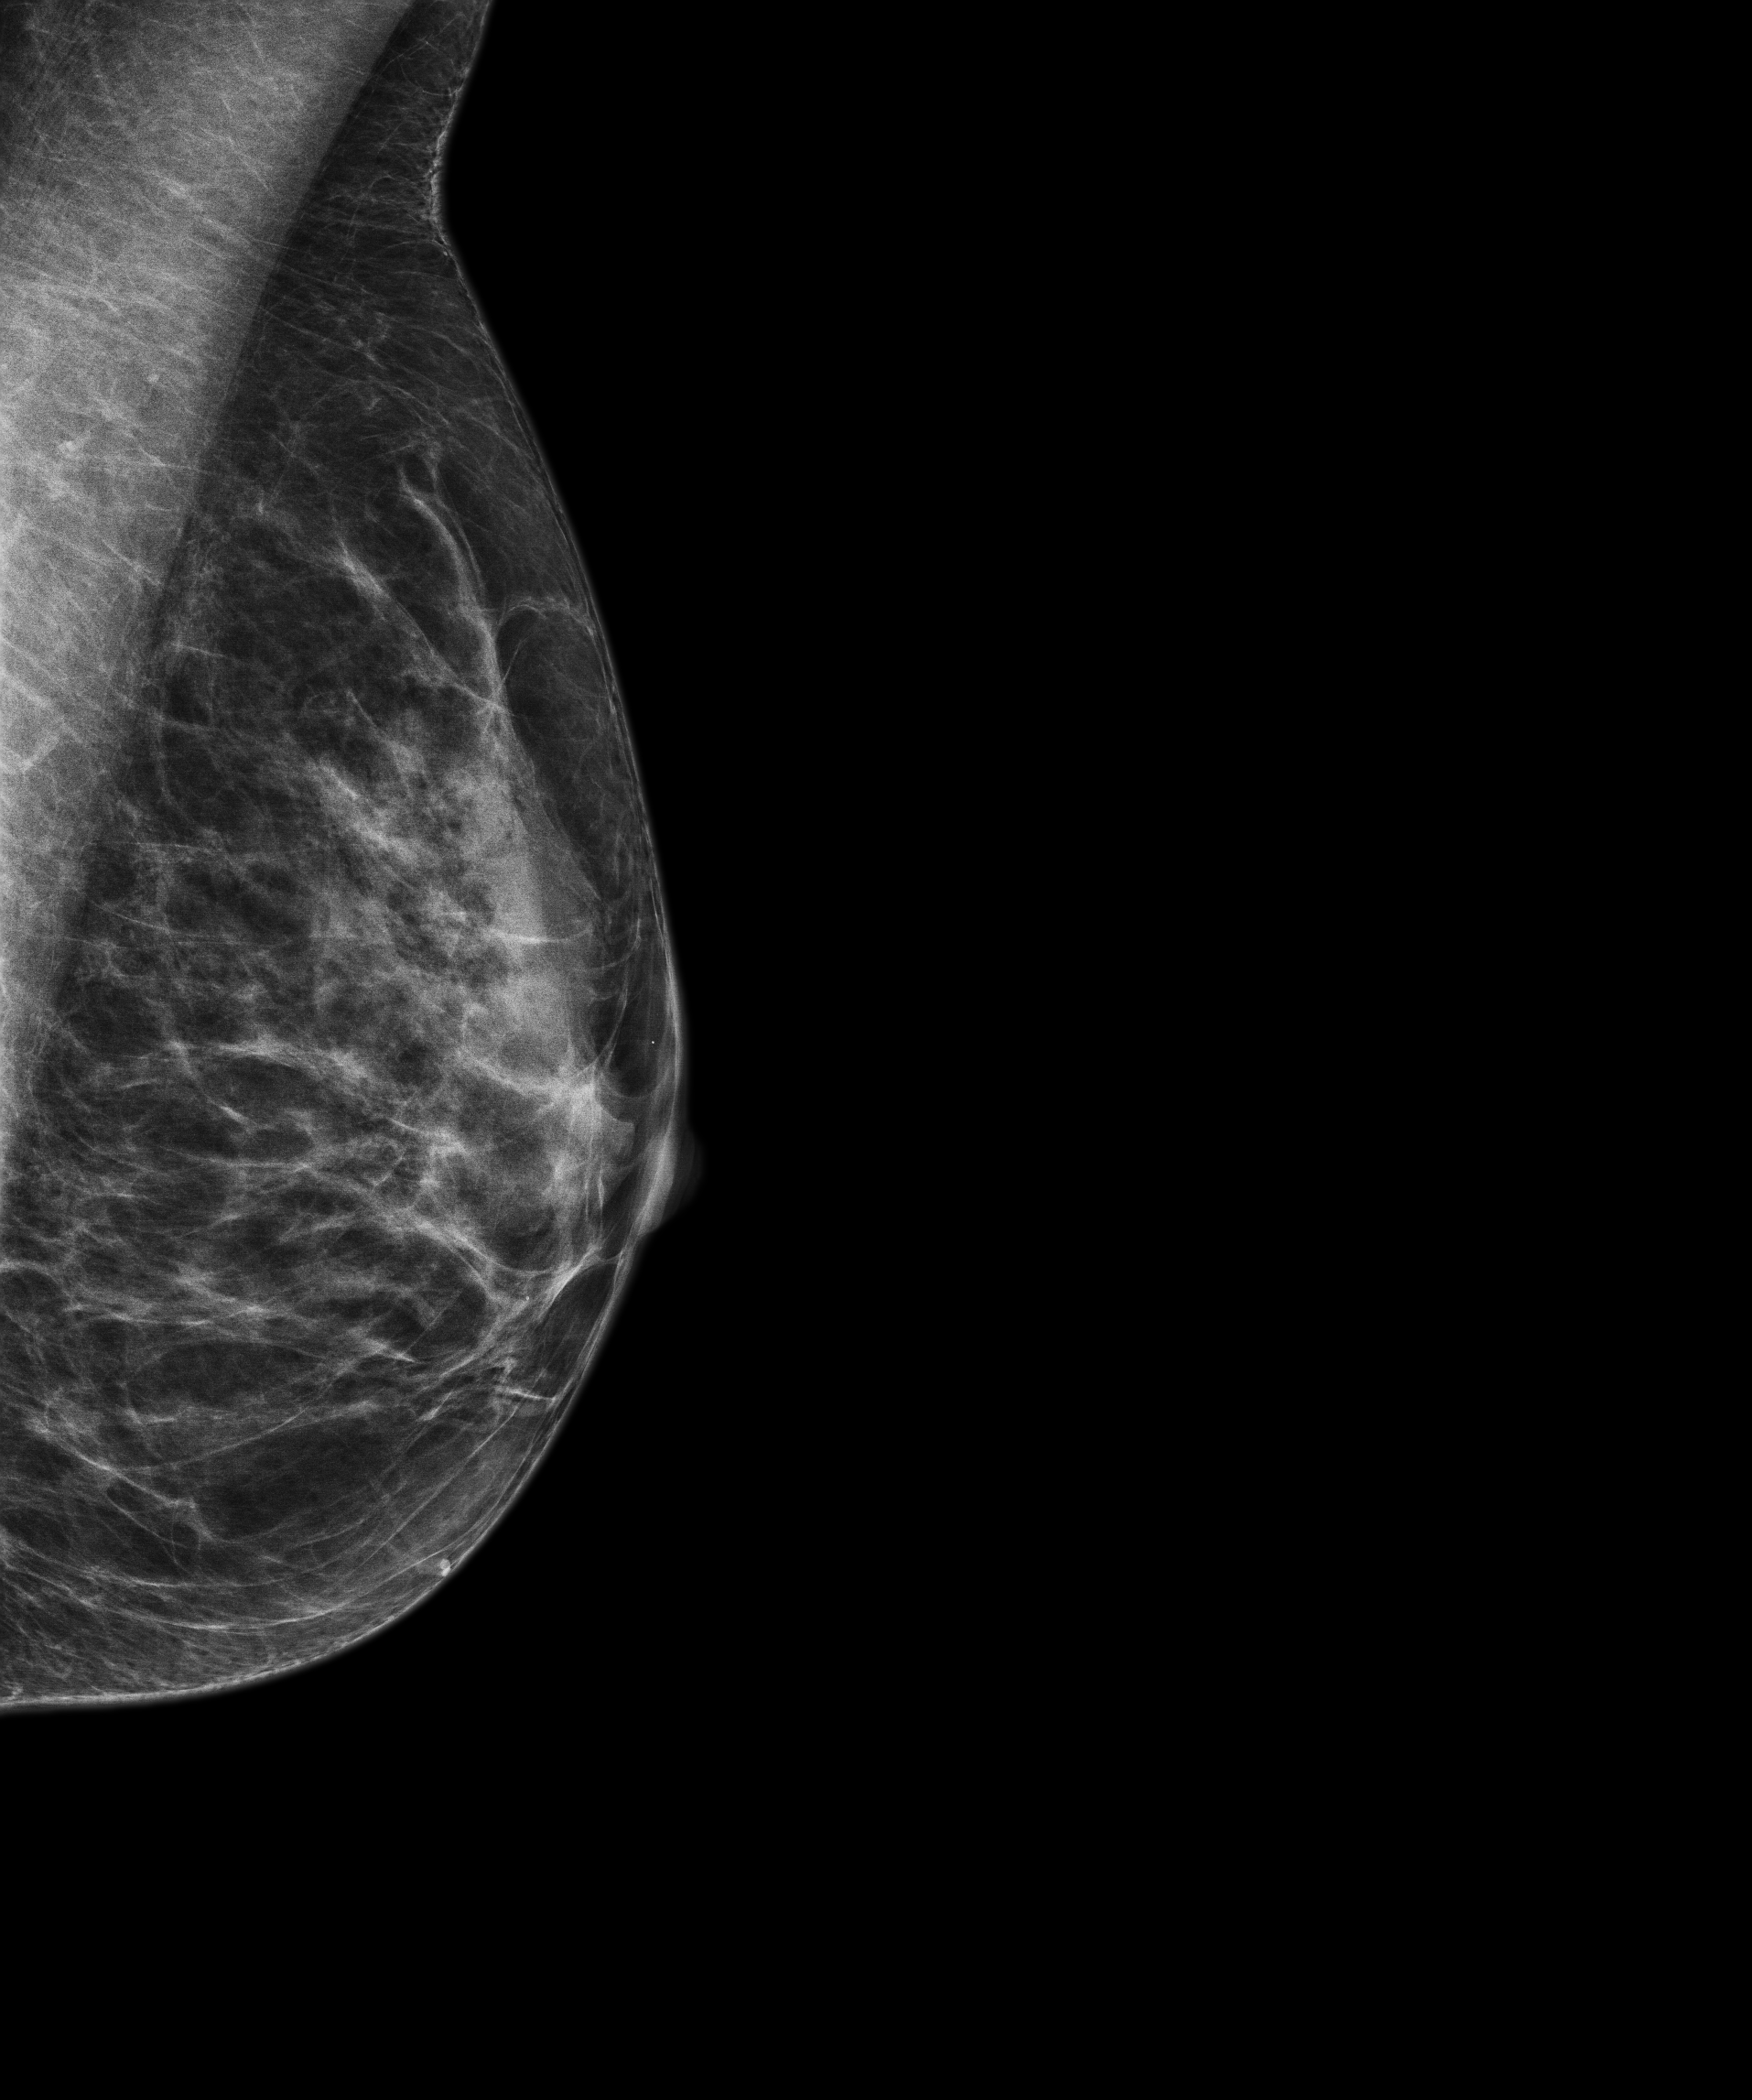
Screening examination, compressed breast thickness 37.9 mm. Female patient, age 66 years.
Image type: full-field digital mammogram. Breast: left. Projection: medio-lateral oblique projection.